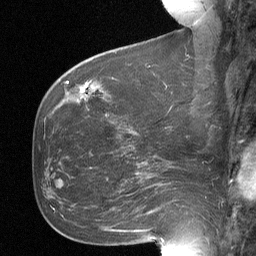
Breast MRI (dynamic contrast-enhanced), one sagittal slice; position 20 of 64 along the scan axis; dynamic contrast-enhanced study with each time point stored as its own series, time point 2 of 3 at this slice position (early post-contrast, ordered by acquisition time); 1.5 T; TE 4.8 ms, TR 27 ms; 2 mm slice thickness; 256 × 256 image matrix. Patient: female, 60 years. From the clinical record (not read from this slice): setting: breast cancer imaged before/during neoadjuvant chemotherapy; receptor status: HR-positive, HER2-negative.
Outlined on this slice (semi-automatic segmentation, software-assisted and operator-edited):
- analysis volume of interest (the breast-tissue region the enhancement analysis was run in; not a lesion): bounding box (x1, y1, x2, y2) in pixels: (67, 68, 109, 111)
- tumour enhancement mask (voxels above the 90 % enhancement threshold inside the analysis volume of interest): (81, 89, 83, 91)